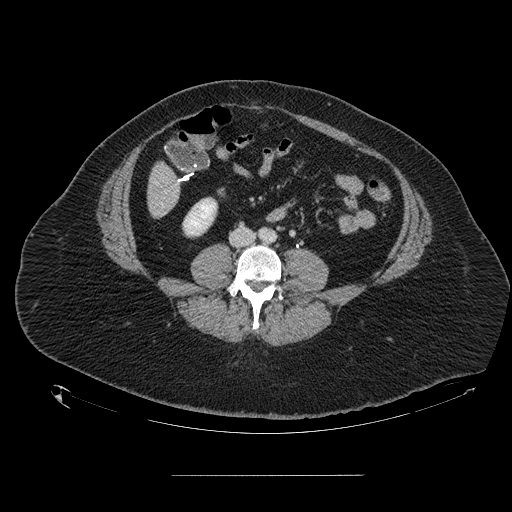
Contrast-enhanced abdominal CT, one axial slice. Position 17 of 164 along the scan axis. 120 kVp. Intravenous contrast given. Soft-tissue window (W 400 / L 40 HU). 2.5 mm slice thickness. 512 × 512 image matrix, field of view 495 × 495 mm. Female patient, age 52 years. Case-level facts recorded for this patient, not image findings: diagnosis: colorectal cancer liver metastases, imaged before liver resection; multiple liver metastases: yes; largest metastasis: 3.5 cm.
Annotated regions visible in this slice (expert manual segmentation):
- liver: bounding box <149,164,179,216> (left, top, right, bottom; pixels)